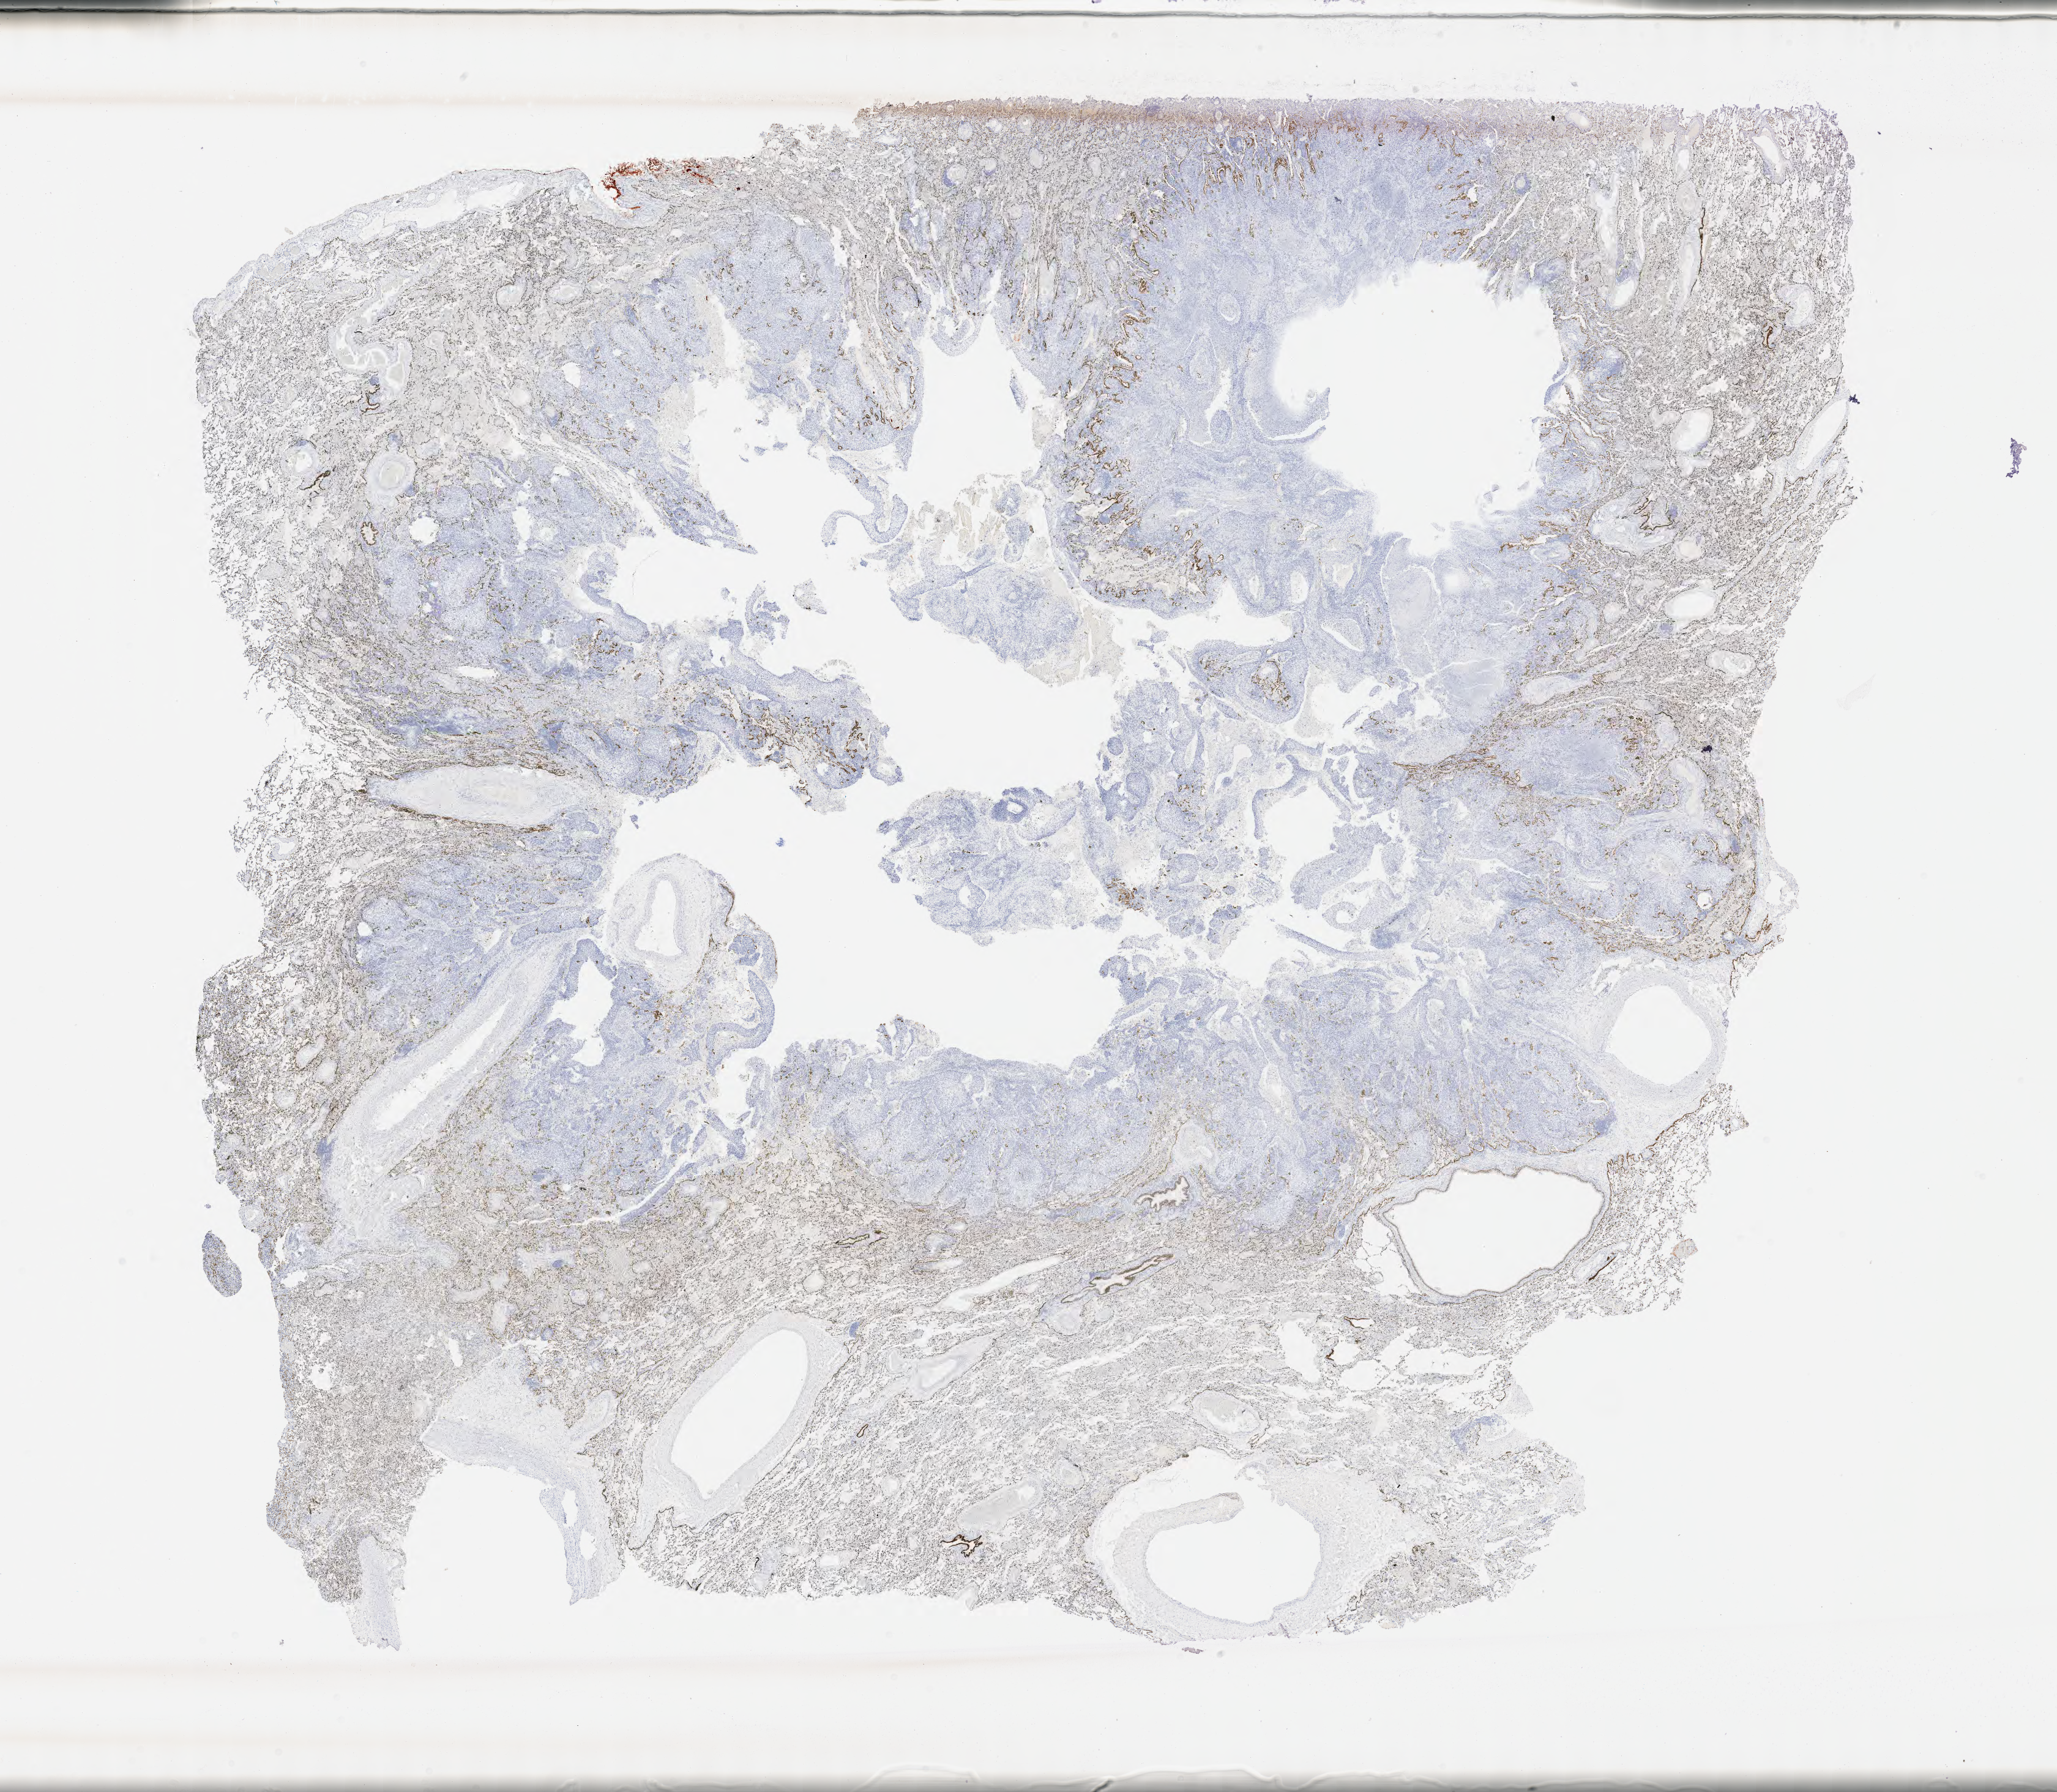
Whole-slide image, immunohistochemical stain for TTF-1 (thyroid transcription factor 1) — low-resolution overview of the scanned area, about 27.2 x 23.7 mm; tumor tissue; anatomic site: lung. Patient sex: male.
Histologic diagnosis: Squamous cell carcinoma, NOS.